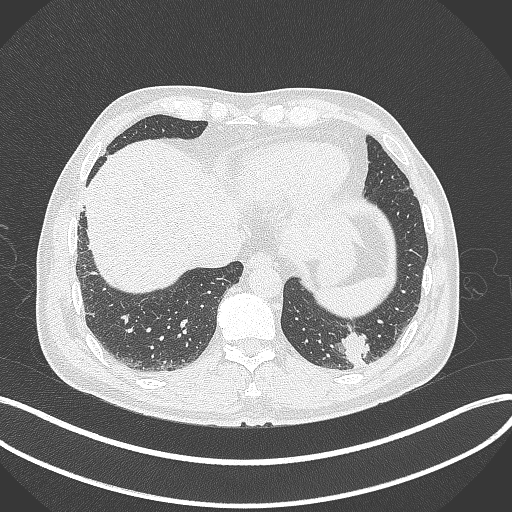
Chest CT, one axial slice; position 59 of 300 along the scan axis; reconstruction kernel B70f; lung window (W 1500 / L -600 HU); 1 mm slice thickness; 512 × 512 image matrix. Male patient, age 54 years. Case-level facts recorded for this patient, not image findings: clinical TNM (as recorded): T1c N0 M1; histopathological grade: G3.
Outlined on this slice (rectangle marked by the reading radiologist):
- lung tumour (recorded histology: adenocarcinoma): bounding box <337,328,371,370> (left, top, right, bottom; pixels)